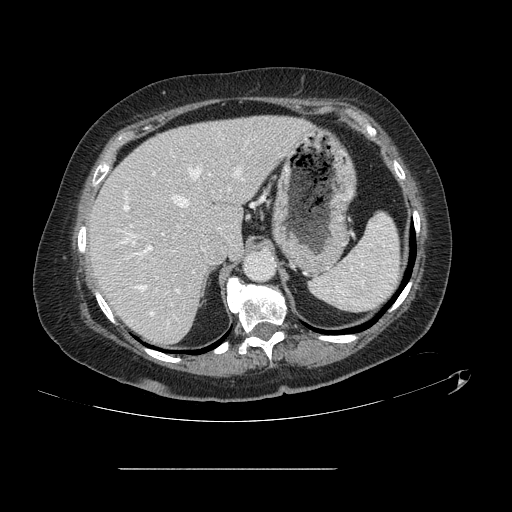
Contrast-enhanced abdominal CT, one axial slice; position 96 of 148 along the scan axis; 120 kVp; intravenous contrast given; soft-tissue window (W 400 / L 40 HU); 2.5 mm slice thickness; 512 × 512 image matrix, field of view 439 × 439 mm. Female patient, age 75 years. From the clinical record (not read from this slice): diagnosis: colorectal cancer liver metastases, imaged before liver resection; multiple liver metastases: no; largest metastasis: 2.4 cm; chemotherapy before resection: no.
Outlined on this slice (manually delineated by an expert):
- hepatic veins: bounding box (x1, y1, x2, y2) in pixels: (133, 168, 244, 315)
- liver: (90, 117, 307, 345)
- planned liver remnant (the part of the liver to remain after resection): (90, 117, 308, 345)
- portal vein (with intrahepatic branches): (124, 141, 248, 292)